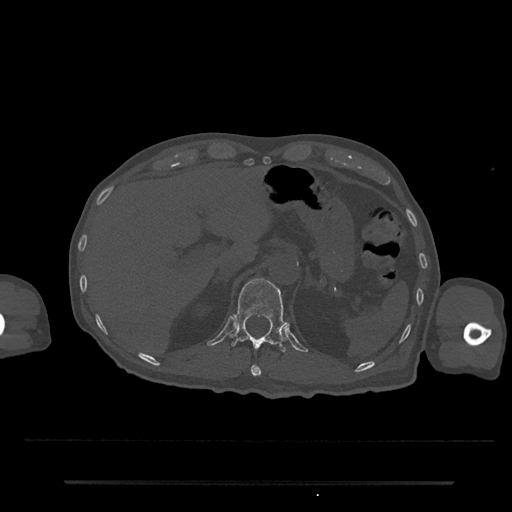
CT including the spine, one axial slice. Slice 200 of 797 in the series (ordered by position). Reconstruction kernel Br40s/3. Bone window (W 1800 / L 400 HU). 0.5 mm slice thickness. 512 × 512 image matrix, field of view 427 × 427 mm. Male patient, age 74 years. Case-level facts recorded for this patient, not image findings: primary cancer: prostate.
Outlined on this slice (semi-automatically segmented with operator editing):
- T11 vertebra: bounding box <250,365,262,377> (left, top, right, bottom; pixels)
- T12 vertebra: <230,278,286,352>